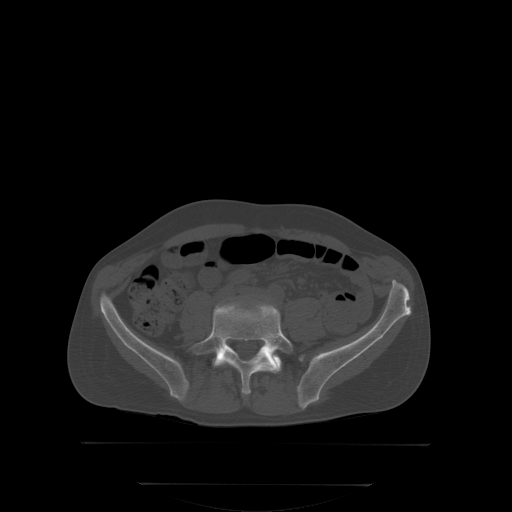
CT including the spine, one axial slice. Position 96 of 350 along the scan axis. Bone window (W 1800 / L 400 HU). 2.5 mm slice thickness. 512 × 512 image matrix, field of view 500 × 500 mm. Male patient, age 58 years. From the clinical record (not read from this slice): primary cancer: prostate; vertebrae with lytic lesions (as recorded): L1.
Structures marked on this image (semi-automatically segmented with operator editing):
- L5 vertebra: bounding box (x1, y1, x2, y2) in pixels: (191, 302, 293, 393)